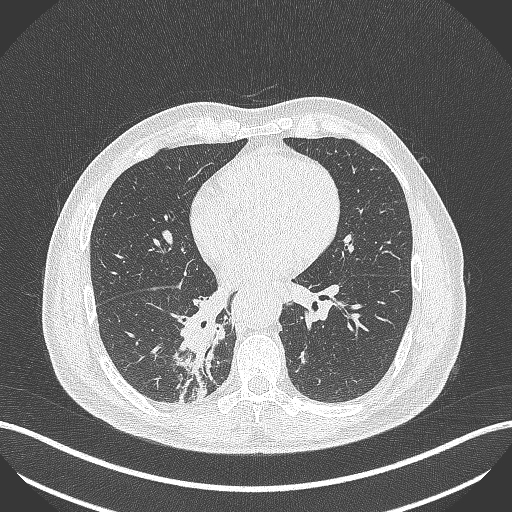
Chest CT, one axial slice; slice 212 of 451 in the series (ordered by position); 100 kVp; lung window (W 1500 / L -600 HU); 1 mm slice thickness; 512 × 512 image matrix, field of view 400 × 400 mm. Patient: male, 61 years. From the clinical record (not read from this slice): clinical TNM (as recorded): T1 N0 M0.
Structures marked on this image (rectangle marked by the reading radiologist):
- lung tumour (recorded histology: small cell carcinoma): bounding box <176,315,216,407> (left, top, right, bottom; pixels)